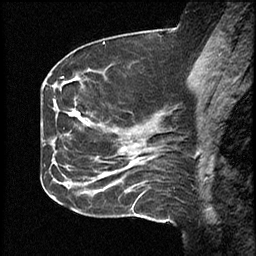
Breast MRI (dynamic contrast-enhanced), one sagittal slice. Slice 21 of 46 in the series (ordered by position). Dynamic contrast-enhanced study with each time point stored as its own series, time point 2 of 4 at this slice position (early post-contrast, ordered by acquisition time). 1.5 T. TE 4.2 ms, TR 18.3 ms. 3 mm slice thickness. 256 × 256 image matrix, field of view 200 × 200 mm. From the clinical record (not read from this slice): setting: breast cancer imaged before/during neoadjuvant chemotherapy; receptor status: HR-positive, HER2-negative.
Annotated regions visible in this slice (semi-automatic segmentation, software-assisted and operator-edited):
- analysis volume of interest (the breast-tissue region the enhancement analysis was run in; not a lesion): bounding box <64,71,111,198> (left, top, right, bottom; pixels)
- tumour enhancement mask (voxels above the 100 % enhancement threshold inside the analysis volume of interest): <73,111,78,116>